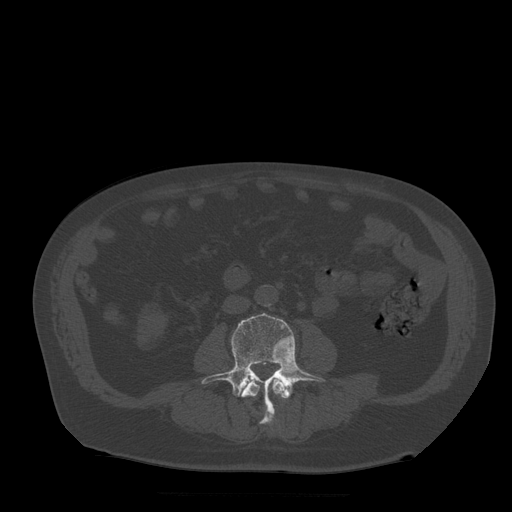
CT including the spine, one axial slice; position 121 of 522 along the scan axis; bone window (W 1800 / L 400 HU); 1.25 mm slice thickness; 512 × 512 image matrix. Patient age 72 years. From the clinical record (not read from this slice): primary cancer: prostate.
Structures marked on this image (semi-automatically segmented with operator editing):
- L3 vertebra: bounding box [x1, y1, x2, y2] px = [242, 378, 289, 425]
- L4 vertebra: [202, 313, 326, 422]